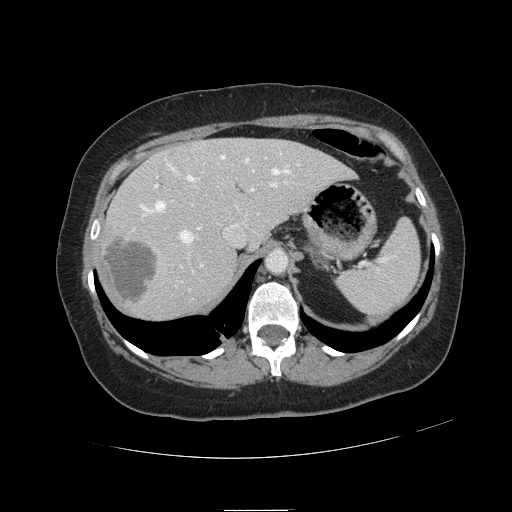
Contrast-enhanced abdominal CT, one axial slice. Slice 83 of 121 in the series (ordered by position). 120 kVp. Intravenous contrast given. Soft-tissue window (W 400 / L 40 HU). 2.5 mm slice thickness. 512 × 512 image matrix. Female patient, age 52 years. Case-level facts recorded for this patient, not image findings: diagnosis: colorectal cancer liver metastases, imaged before liver resection; multiple liver metastases: yes; largest metastasis: 6.3 cm; disease in both lobes: no.
Outlined on this slice (expert manual segmentation):
- hepatic veins: bounding box (x1, y1, x2, y2) in pixels: (141, 153, 290, 243)
- liver: (101, 138, 351, 317)
- planned liver remnant (the part of the liver to remain after resection): (168, 138, 351, 244)
- portal vein (with intrahepatic branches): (154, 158, 287, 291)
- liver metastasis: (105, 237, 157, 304)